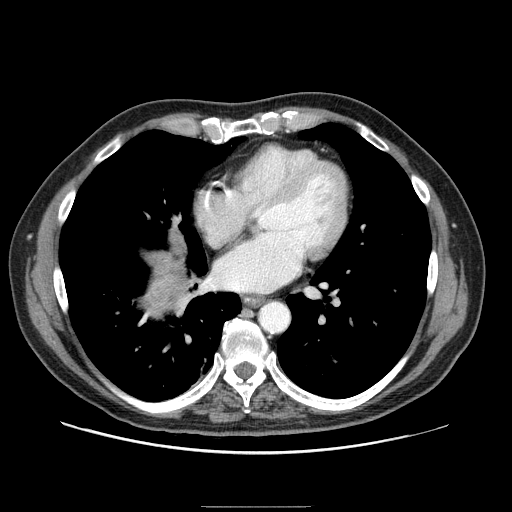
Contrast-enhanced abdominal CT (liver protocol), one axial slice. Position 90 of 99 along the scan axis. Reconstruction kernel STANDARD. One of 2 acquisitions stored at this slice position. Soft-tissue window (W 400 / L 40 HU). 512 × 512 image matrix. Case-level facts recorded for this patient, not image findings: diagnosis: hepatocellular carcinoma (patient treated with transarterial chemoembolisation; whether this scan precedes or follows treatment is not stated here); TNM stage (as recorded): Stage-II.
Structures marked on this image (semi-automatically segmented with operator editing):
- liver parenchyma outside the tumour (the mass and vessels are separate outlines, so this box may not span the whole liver): bounding box (x1, y1, x2, y2) in pixels: (146, 258, 184, 312)